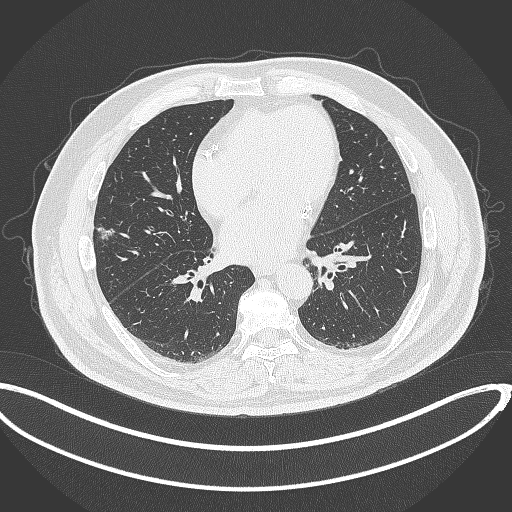
Chest CT, one axial slice. Slice 141 of 340 in the series (ordered by position). 120 kVp. Lung window (W 1500 / L -600 HU). 1 mm slice thickness. 512 × 512 image matrix, field of view 427 × 427 mm. Patient: male, 68 years. From the clinical record (not read from this slice): clinical TNM (as recorded): T1c N0 M0.
Outlined on this slice (bounding box drawn by a radiologist):
- lung tumour (recorded histology: adenocarcinoma): box from (x=97, y=224) to (x=117, y=242) px